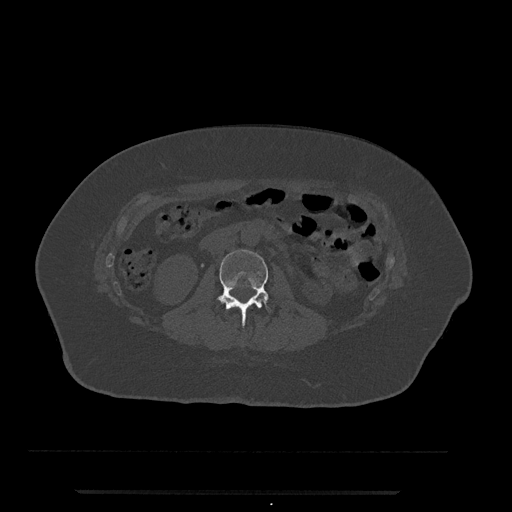
CT including the spine, one axial slice; position 35 of 797 along the scan axis; reconstruction kernel Br40s/3; 120 kVp; bone window (W 1800 / L 400 HU); 0.5 mm slice thickness; 512 × 512 image matrix. Patient: female, 51 years. Case-level facts recorded for this patient, not image findings: primary cancer: neuro.
Structures marked on this image (semi-automatically segmented with operator editing):
- L2 vertebra: bounding box (x1, y1, x2, y2) in pixels: (217, 249, 271, 326)